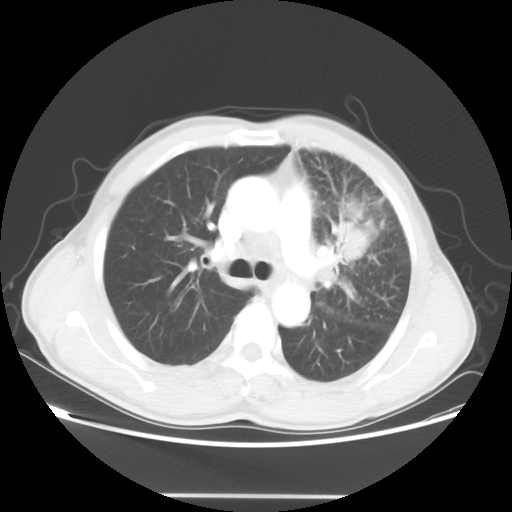
Chest CT, one axial slice. Position 34 of 55 along the scan axis. Reconstruction kernel STANDARD. 100 kVp. Lung window (W 1500 / L -600 HU). 512 × 512 image matrix, field of view 398 × 398 mm. Male patient, age 60 years. Case-level facts recorded for this patient, not image findings: clinical TNM (as recorded): T3 N3 M0.
Structures marked on this image (rectangle marked by the reading radiologist):
- lung tumour (recorded histology: adenocarcinoma): bounding box [x1, y1, x2, y2] px = [340, 216, 369, 261]